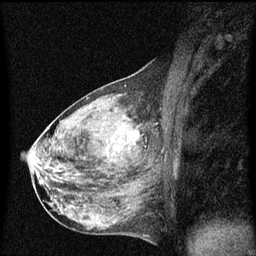
Breast MRI (dynamic contrast-enhanced), one sagittal slice; position 30 of 60 along the scan axis; dynamic contrast-enhanced series, image 2 of 3 at this slice position (ordered by acquisition); 1.5 T; TE 4.2 ms, TR 8 ms; 256 × 256 image matrix, field of view 200 × 200 mm. Female patient, age 50 years.
Annotated regions visible in this slice (semi-automatically segmented with operator editing):
- analysis volume of interest (the breast-tissue region the enhancement analysis was run in; not a lesion): box from (x=106, y=118) to (x=148, y=159) px
- tumour enhancement mask (voxels above the 70 % enhancement threshold inside the analysis volume of interest): (x=129, y=130)–(x=139, y=143)